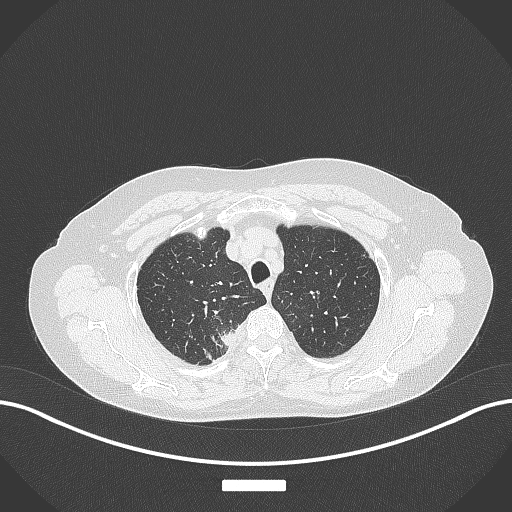
Chest CT, one axial slice. Slice 323 of 357 in the series (ordered by position). Reconstruction kernel B70f. 120 kVp. Lung window (W 1500 / L -600 HU). 1 mm slice thickness. 512 × 512 image matrix, field of view 400 × 400 mm. Female patient, age 62 years. From the clinical record (not read from this slice): clinical TNM (as recorded): T1c N1 M0.
Structures marked on this image (rectangle marked by the reading radiologist):
- lung tumour (recorded histology: squamous cell carcinoma): bounding box <214,325,238,346> (left, top, right, bottom; pixels)